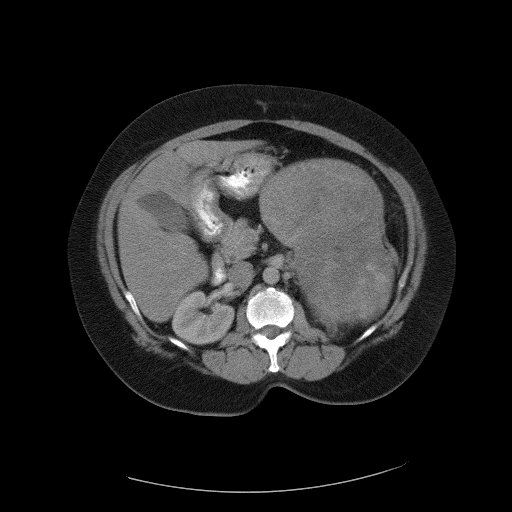
Contrast-enhanced abdominal CT, one axial slice; position 62 of 90 along the scan axis; reconstruction kernel FC01; intravenous contrast given; soft-tissue window (W 400 / L 40 HU); 5 mm slice thickness; 512 × 512 image matrix, field of view 480 × 480 mm. Patient: female, 55 years. From the clinical record (not read from this slice): diagnosis: adrenocortical carcinoma; tumour side: left adrenal; tumour size at pathology: 22 cm; Ki-67 index: 10 %.
Outlined on this slice (semi-automatically segmented with operator editing):
- mass: bounding box (x1, y1, x2, y2) in pixels: (262, 159, 393, 322)